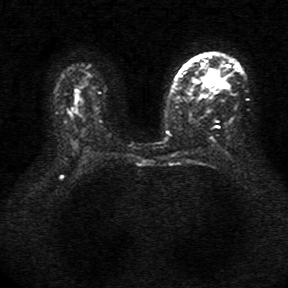
Breast MRI, one axial slice. Position 23 of 34 along the scan axis. Diffusion-weighted series; image 2 of 4 stored at this slice position (different b-values; order by instance number). 1.5 T. 5 mm slice thickness. 288 × 288 image matrix. Female patient.
Structures marked on this image (expert manual segmentation):
- tumour on diffusion-weighted imaging: bounding box [x1, y1, x2, y2] px = [207, 74, 217, 84]